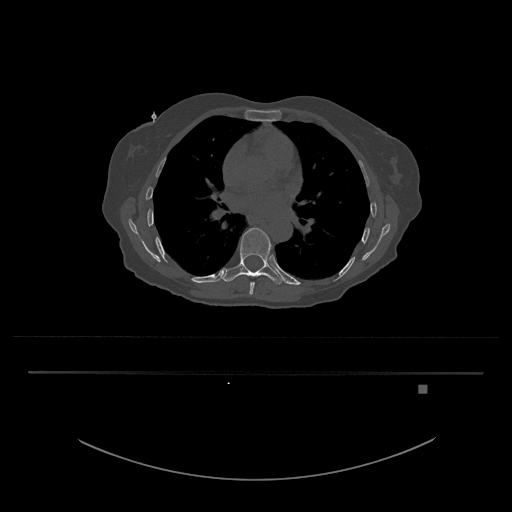
CT including the spine, one axial slice. 120 kVp. Bone window (W 1800 / L 400 HU). 0.5 mm slice thickness. 512 × 512 image matrix, field of view 500 × 500 mm. Patient: female, 57 years. From the clinical record (not read from this slice): primary cancer: cervical.
Annotated regions visible in this slice (semi-automatic segmentation, software-assisted and operator-edited):
- T8 vertebra: bounding box [x1, y1, x2, y2] px = [249, 281, 255, 295]
- T9 vertebra: [222, 228, 284, 285]